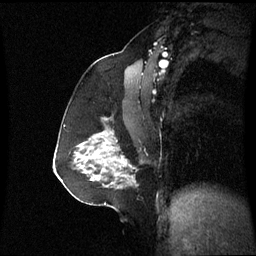
Breast MRI (dynamic contrast-enhanced), one sagittal slice; dynamic contrast-enhanced series, image 2 of 3 at this slice position (ordered by acquisition); 1.5 T; TE 4.2 ms, TR 8.9 ms; 256 × 256 image matrix. Female patient, age 59 years. Case-level facts recorded for this patient, not image findings: setting: breast cancer imaged before/during neoadjuvant chemotherapy; receptor status: triple-negative.
Structures marked on this image (semi-automatic segmentation, software-assisted and operator-edited):
- analysis volume of interest (the breast-tissue region the enhancement analysis was run in; not a lesion): bounding box (x1, y1, x2, y2) in pixels: (86, 128, 135, 183)
- tumour enhancement mask (voxels above the 70 % enhancement threshold inside the analysis volume of interest): (119, 159, 125, 163)